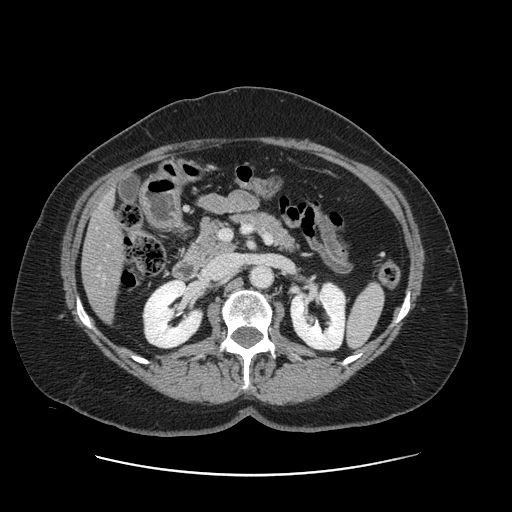
Contrast-enhanced abdominal CT, one axial slice; position 60 of 161 along the scan axis; 120 kVp; soft-tissue window (W 400 / L 40 HU); 2.5 mm slice thickness; 512 × 512 image matrix, field of view 398 × 398 mm. Female patient, age 62 years. Case-level facts recorded for this patient, not image findings: diagnosis: colorectal cancer liver metastases, imaged before liver resection; multiple liver metastases: no; largest metastasis: 2.5 cm.
Outlined on this slice (manually delineated by an expert):
- liver: bounding box [x1, y1, x2, y2] px = [83, 194, 123, 319]